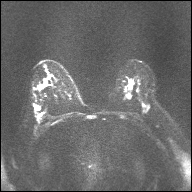
Breast MRI, one axial slice. Position 21 of 32 along the scan axis. Diffusion-weighted series; image 2 of 4 stored at this slice position (different b-values; order by instance number). 1.5 T. 4 mm slice thickness. 192 × 192 image matrix, field of view 360 × 360 mm. Female patient.
Structures marked on this image (outlined manually by an expert reader):
- tumour on diffusion-weighted imaging: bounding box (x1, y1, x2, y2) in pixels: (44, 79, 46, 86)